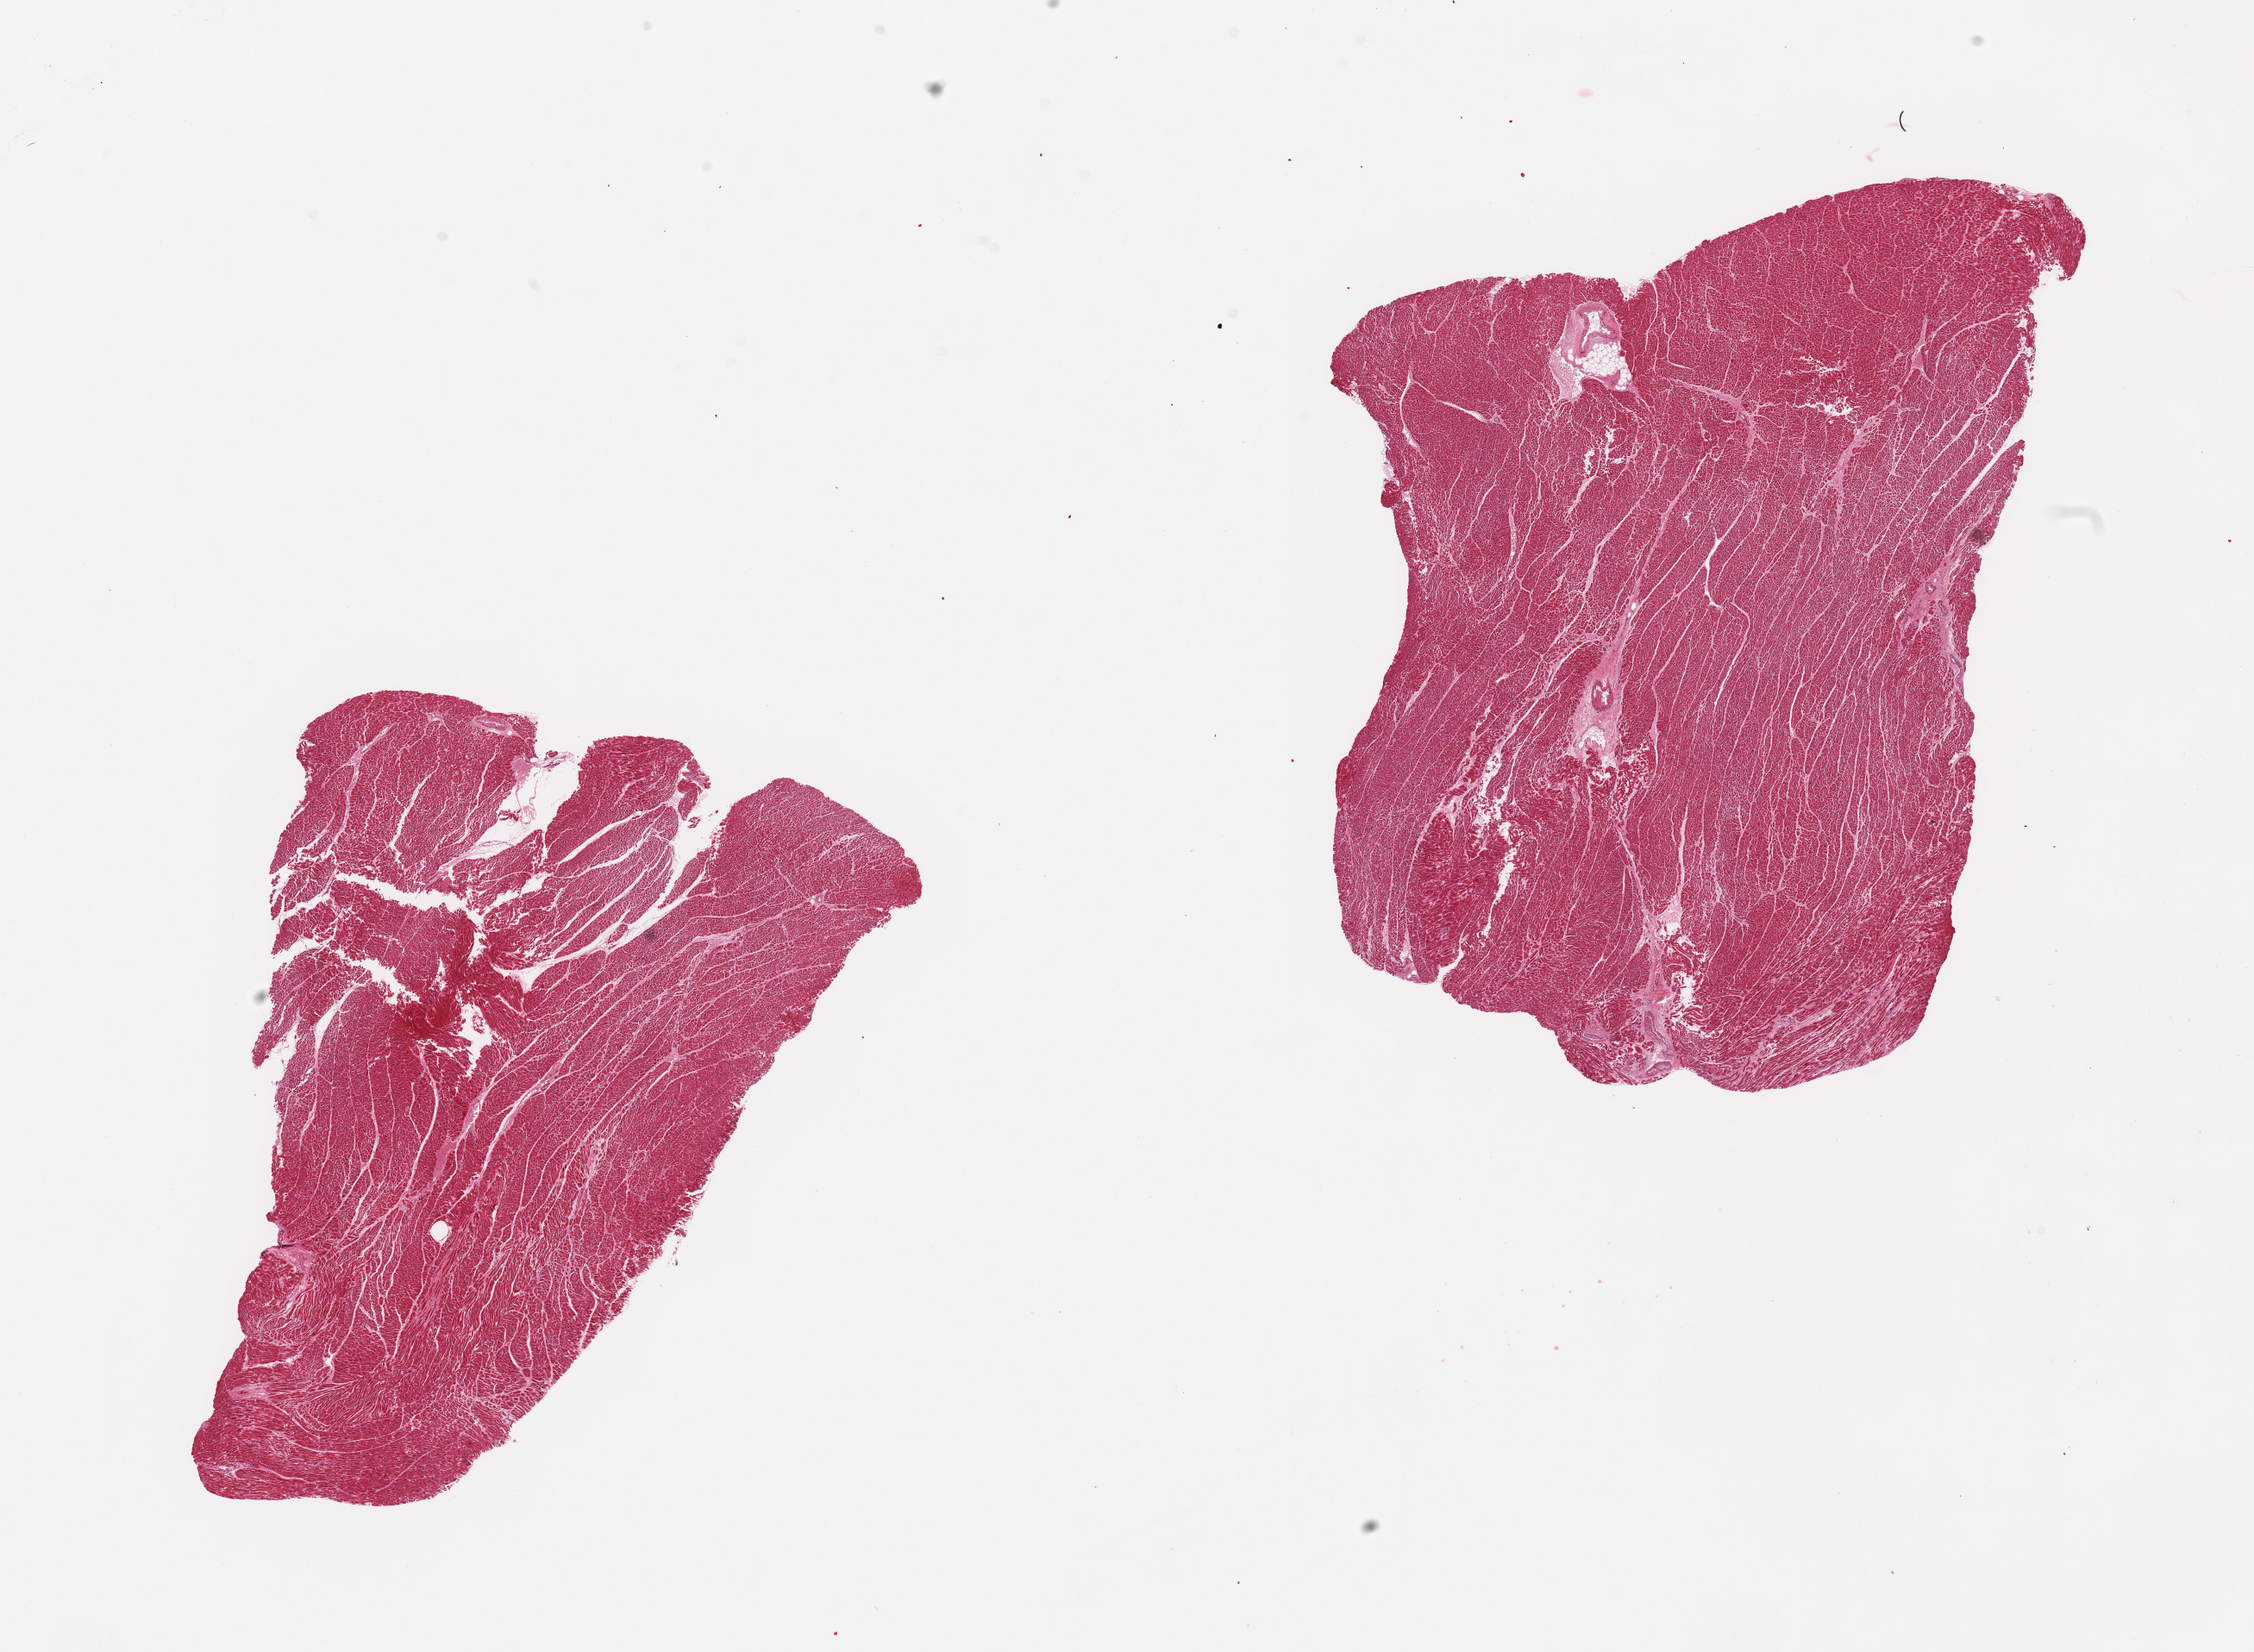
Whole-slide image, haematoxylin and eosin stain, brightfield, whole scanned area (about 20.7 x 15.2 mm) shown as a low-resolution overview; PAXgene-fixed, paraffin-embedded tissue; target tissue: heart; donor tissue sample. Donor sex: male.
- reviewer comment on this tissue sample: 2 pieces, mild interstitial fibrosis/chronic ischemic changes